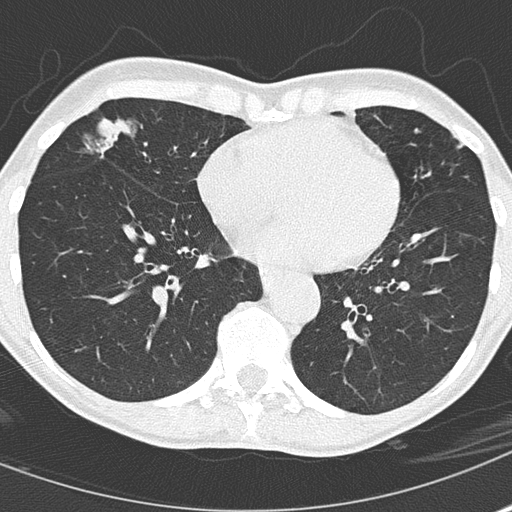
Low-dose screening chest CT, axial slice, second annual screen, lung window (W 1500 / L -600 HU), 512 × 512 image matrix. Female, age 67 years at enrolment. Current smoker at enrolment.
Expert reader's lesion annotation, bounding box <84,108,191,198> (left, top, right, bottom; pixels). The screening reader recorded 2 non-calcified nodules or masses ≥4 mm on this exam (right middle lobe, right middle lobe); which of them this box marks is not recorded.